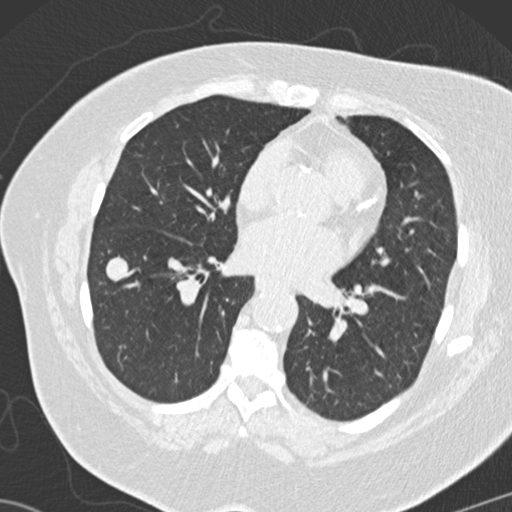
Low-dose screening chest CT, one axial slice. Slice 64 of 146 in the series (ordered by position). 120 kVp. Lung window (W 1500 / L -600 HU). 2 mm slice thickness. 512 × 512 image matrix, field of view 350 × 350 mm.
Outlined on this slice (outlined manually by an expert reader):
- lesion 2 (tumor, lower lobe of right lung): box from (x=106, y=254) to (x=129, y=281) px